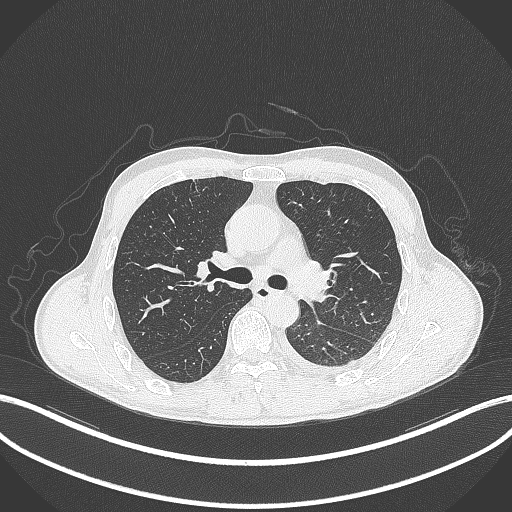
Chest CT, one axial slice. Slice 210 of 295 in the series (ordered by position). Lung window (W 1500 / L -600 HU). 1 mm slice thickness. 512 × 512 image matrix. Patient: male, 47 years. From the clinical record (not read from this slice): clinical TNM (as recorded): T3 N1 M1c.
Structures marked on this image (rectangle marked by the reading radiologist):
- lung tumour (recorded histology: small cell carcinoma): bounding box [x1, y1, x2, y2] px = [302, 286, 330, 303]